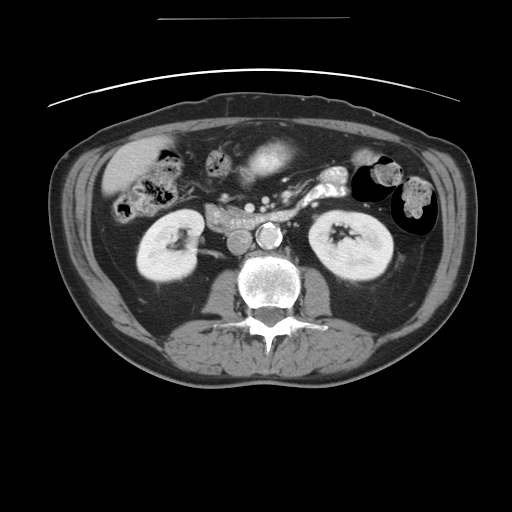
Contrast-enhanced abdominal CT, one axial slice; position 13 of 49 along the scan axis; 120 kVp; soft-tissue window (W 400 / L 40 HU); 512 × 512 image matrix, field of view 413 × 413 mm. Male patient, age 57 years. Case-level facts recorded for this patient, not image findings: diagnosis: colorectal cancer liver metastases, imaged before liver resection; multiple liver metastases: yes; largest metastasis: 4 cm; disease in both lobes: no.
Annotated regions visible in this slice (outlined manually by an expert reader):
- liver: bounding box (x1, y1, x2, y2) in pixels: (103, 137, 166, 193)